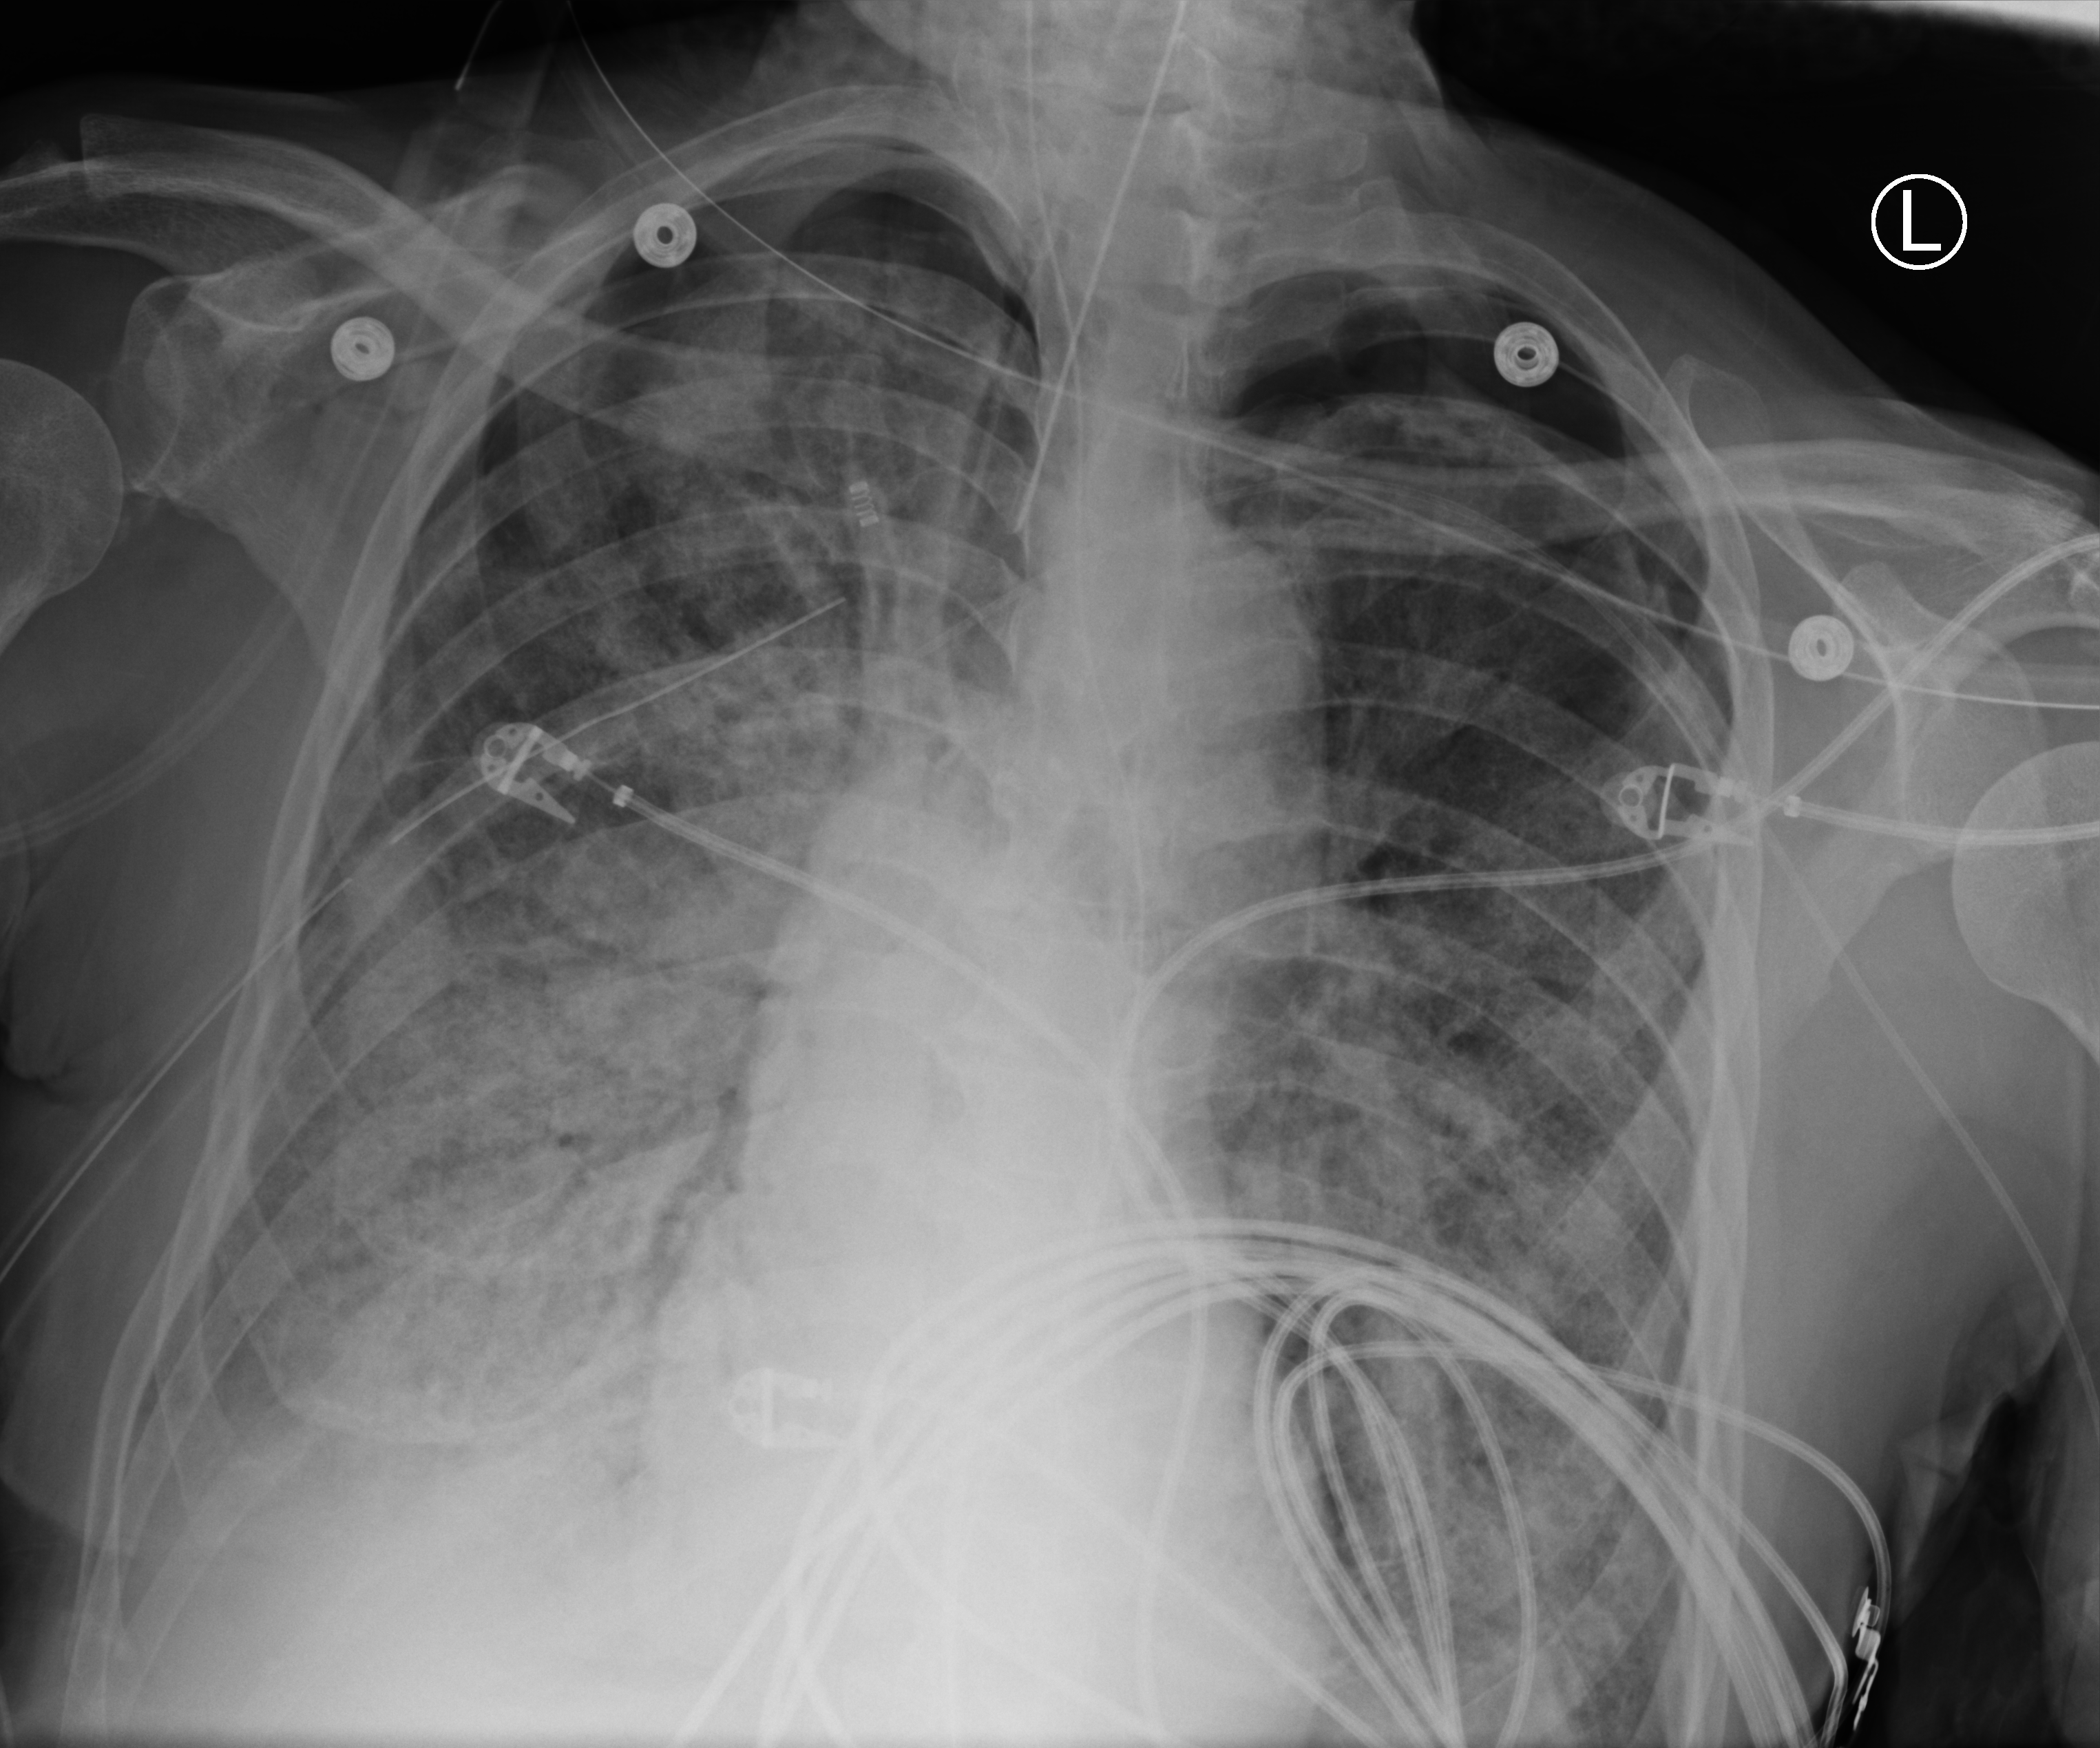
Portable chest radiograph. Patient hospitalised with COVID-19; male, aged 60–74 years.
From the hospital-stay record, not from the radiograph (when in the stay this image was taken is not recorded): mechanically ventilated during this hospital stay: yes; diabetes (admission record): no.